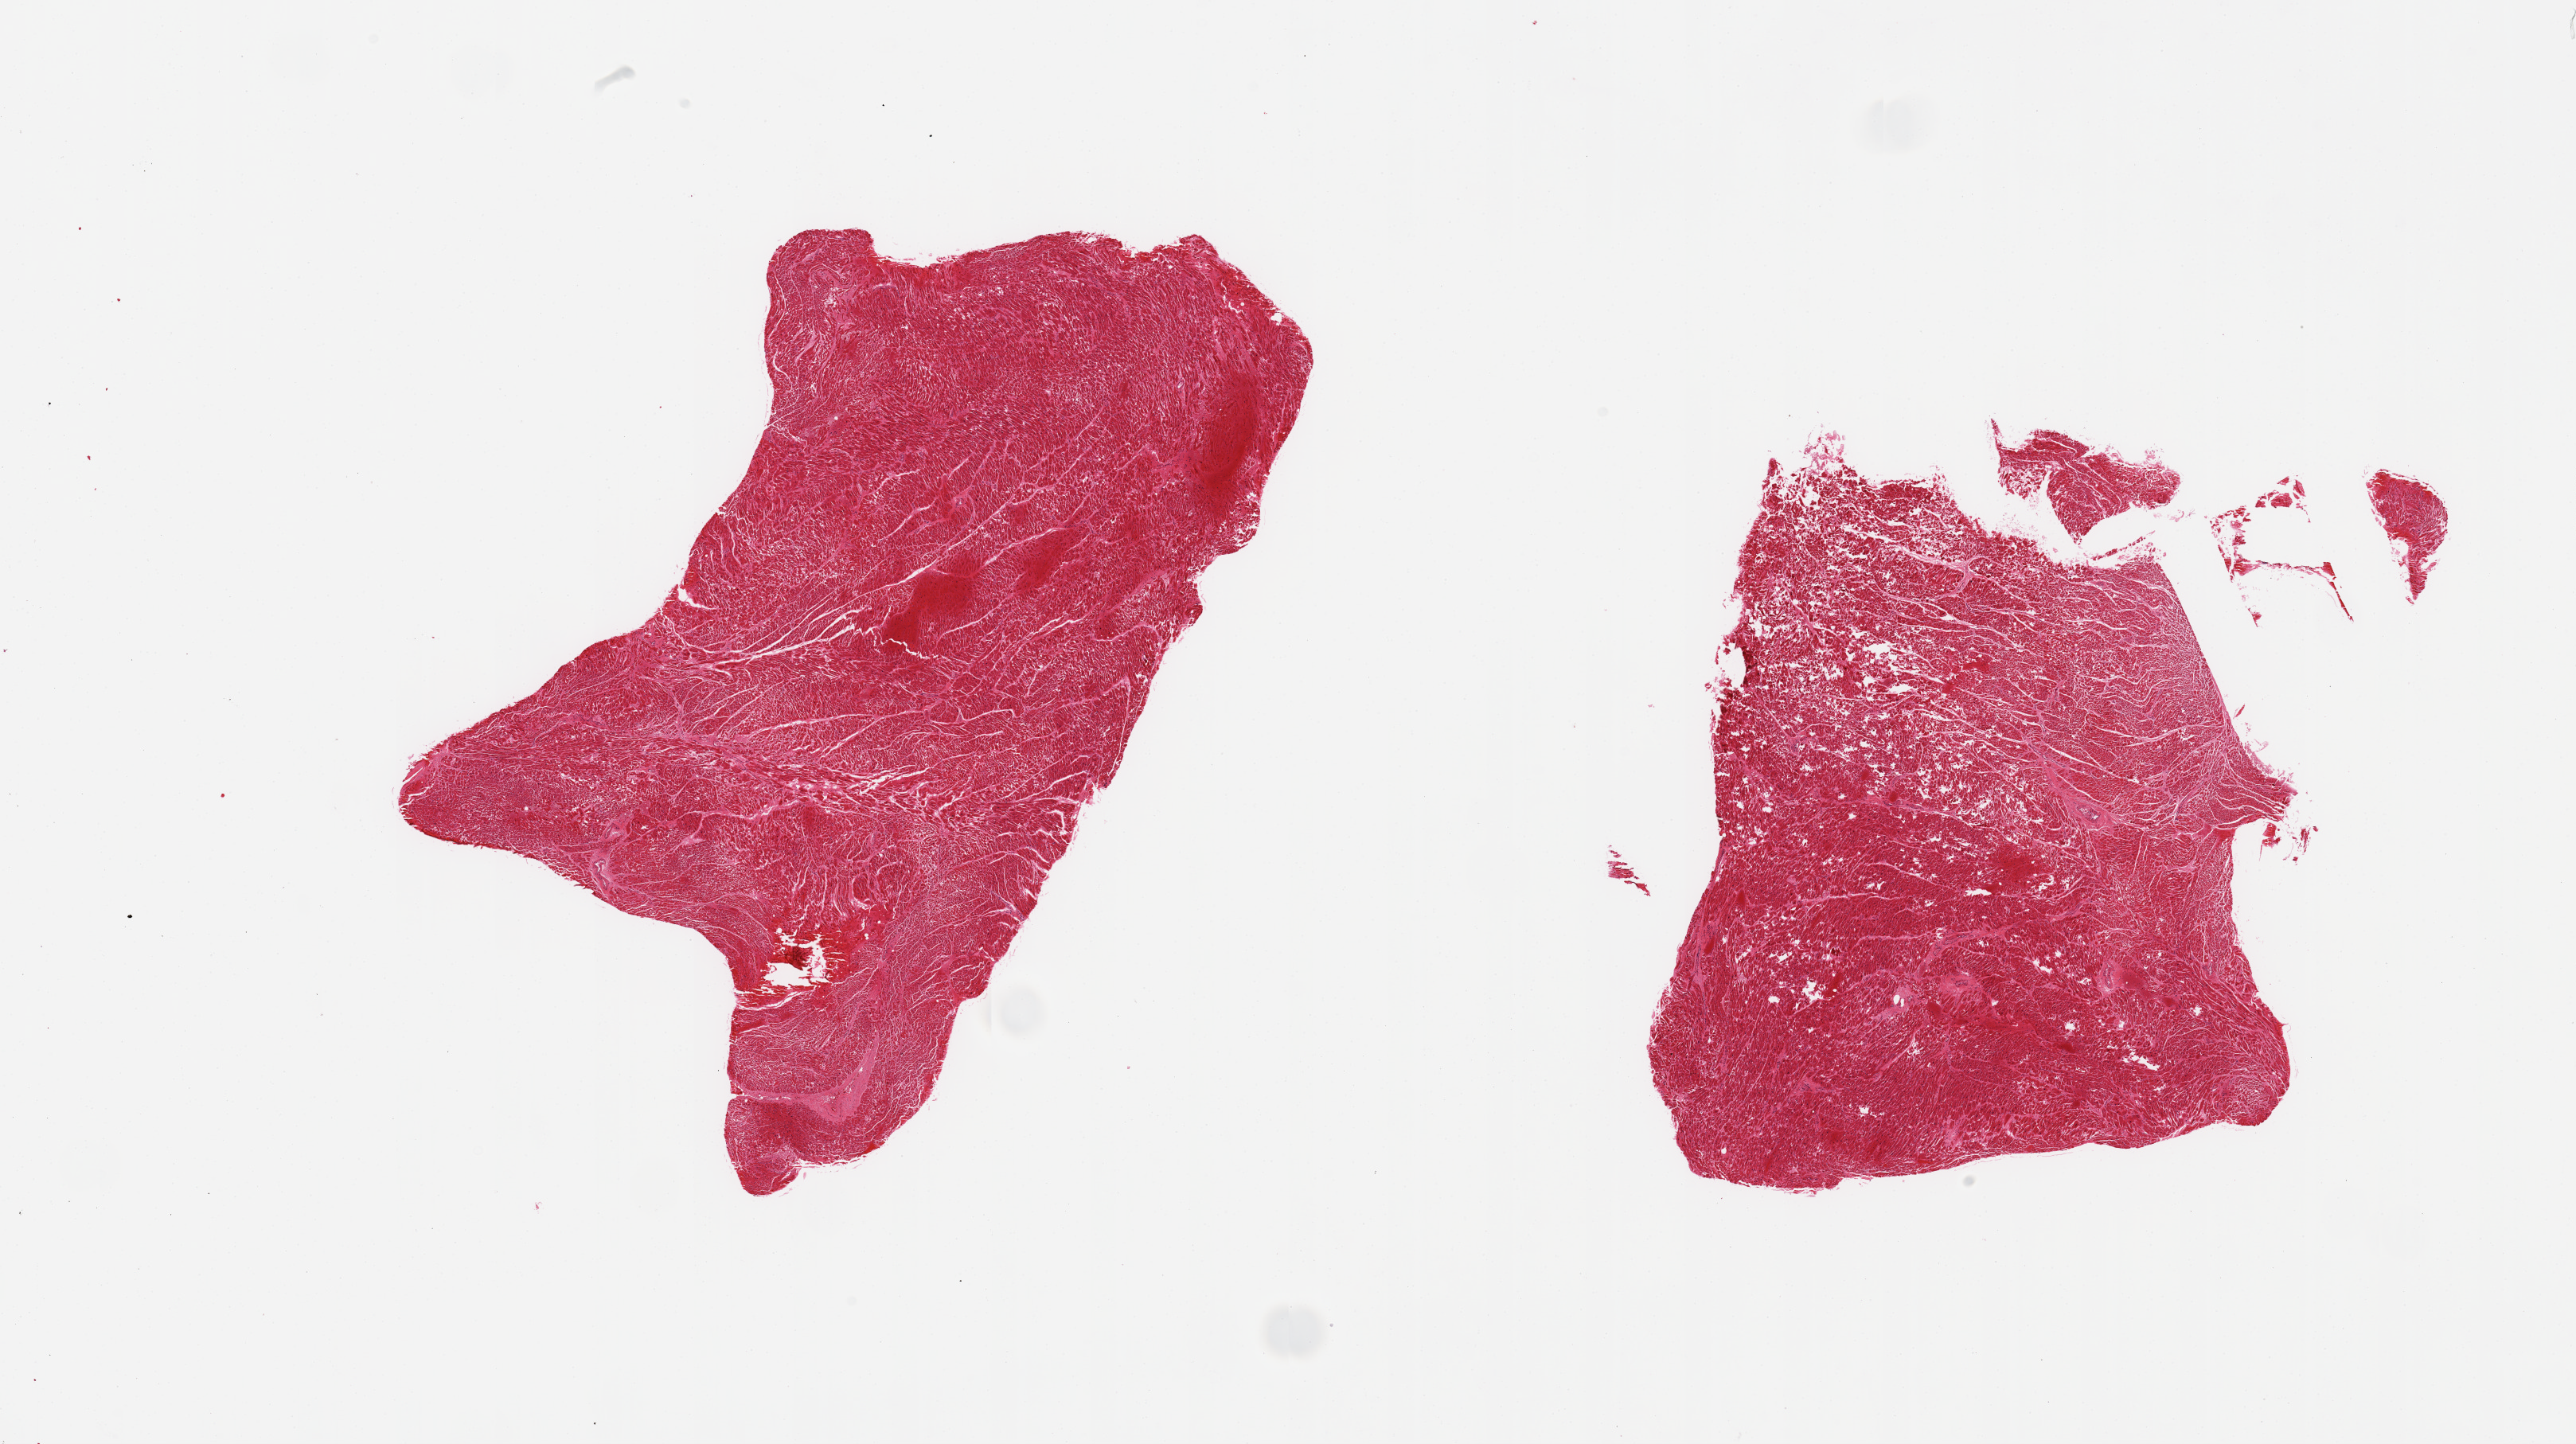
Whole-slide image, H&E stain — low-resolution overview of the scanned area, about 25.6 x 14.3 mm. PAXgene-fixed, paraffin-embedded tissue. Sampled site (target tissue): heart. Tissue donor sample.
* pathologist's review note for this sample: 2 pieces; patchy hypereosinophilia and hemorrhage consistent with recent myocardial infarction